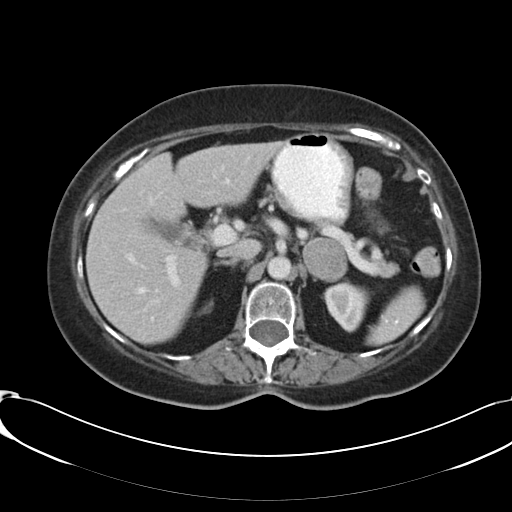
Contrast-enhanced abdominal CT, one axial slice. Position 70 of 91 along the scan axis. Reconstruction kernel B30f. Intravenous contrast given. Soft-tissue window (W 400 / L 40 HU). 5 mm slice thickness. 512 × 512 image matrix, field of view 366 × 366 mm. Patient: female, 73 years. Case-level facts recorded for this patient, not image findings: diagnosis: adrenocortical carcinoma; tumour side: left adrenal; tumour size at pathology: 4.9 cm; Ki-67 index: 10 %; stage (as recorded): 3.
Structures marked on this image (semi-automatically segmented with operator editing):
- mass: bounding box [x1, y1, x2, y2] px = [304, 239, 346, 281]